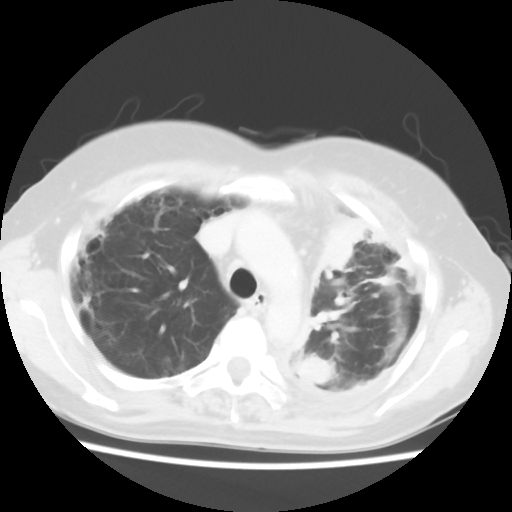
Chest CT, one axial slice; slice 41 of 56 in the series (ordered by position); reconstruction kernel STANDARD; 120 kVp; lung window (W 1500 / L -600 HU); 5 mm slice thickness; 512 × 512 image matrix. Patient: female, 56 years. From the clinical record (not read from this slice): clinical TNM (as recorded): T1c N0 M1.
Outlined on this slice (rectangle marked by the reading radiologist):
- lung tumour (recorded histology: adenocarcinoma): box from (x=316, y=215) to (x=374, y=280) px